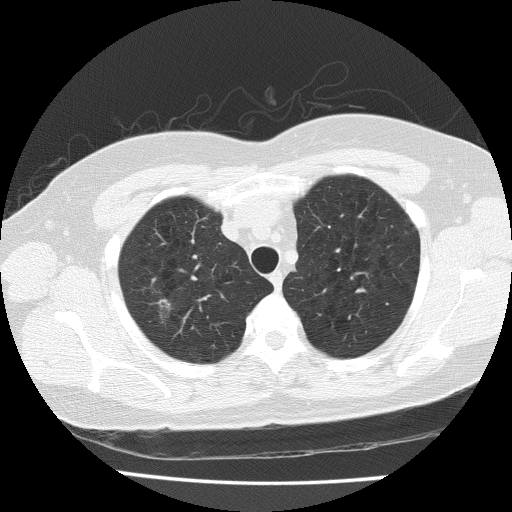
Low-dose screening chest CT, axial slice; first (baseline) screen; lung window (W 1500 / L -600 HU); 2 mm slice thickness; slice 32 of 175 in the series; 512 × 512 image matrix. Female participant, aged 57 years at enrolment. Former smoker at enrolment.
Expert reader's lesion annotation, bounding box [x1, y1, x2, y2] px = [134, 286, 180, 331]. Reader record for this screening exam (exam-level; its link to the box is not recorded): non-calcified nodule or mass ≥4 mm, right upper lobe, 8 × 7 mm, spiculated (stellate) margins, soft tissue attenuation. Official screen result: positive, change unspecified: nodule(s) >= 4 mm or enlarging nodule(s), mass(es), or other non-specific abnormalities suspicious for lung cancer.